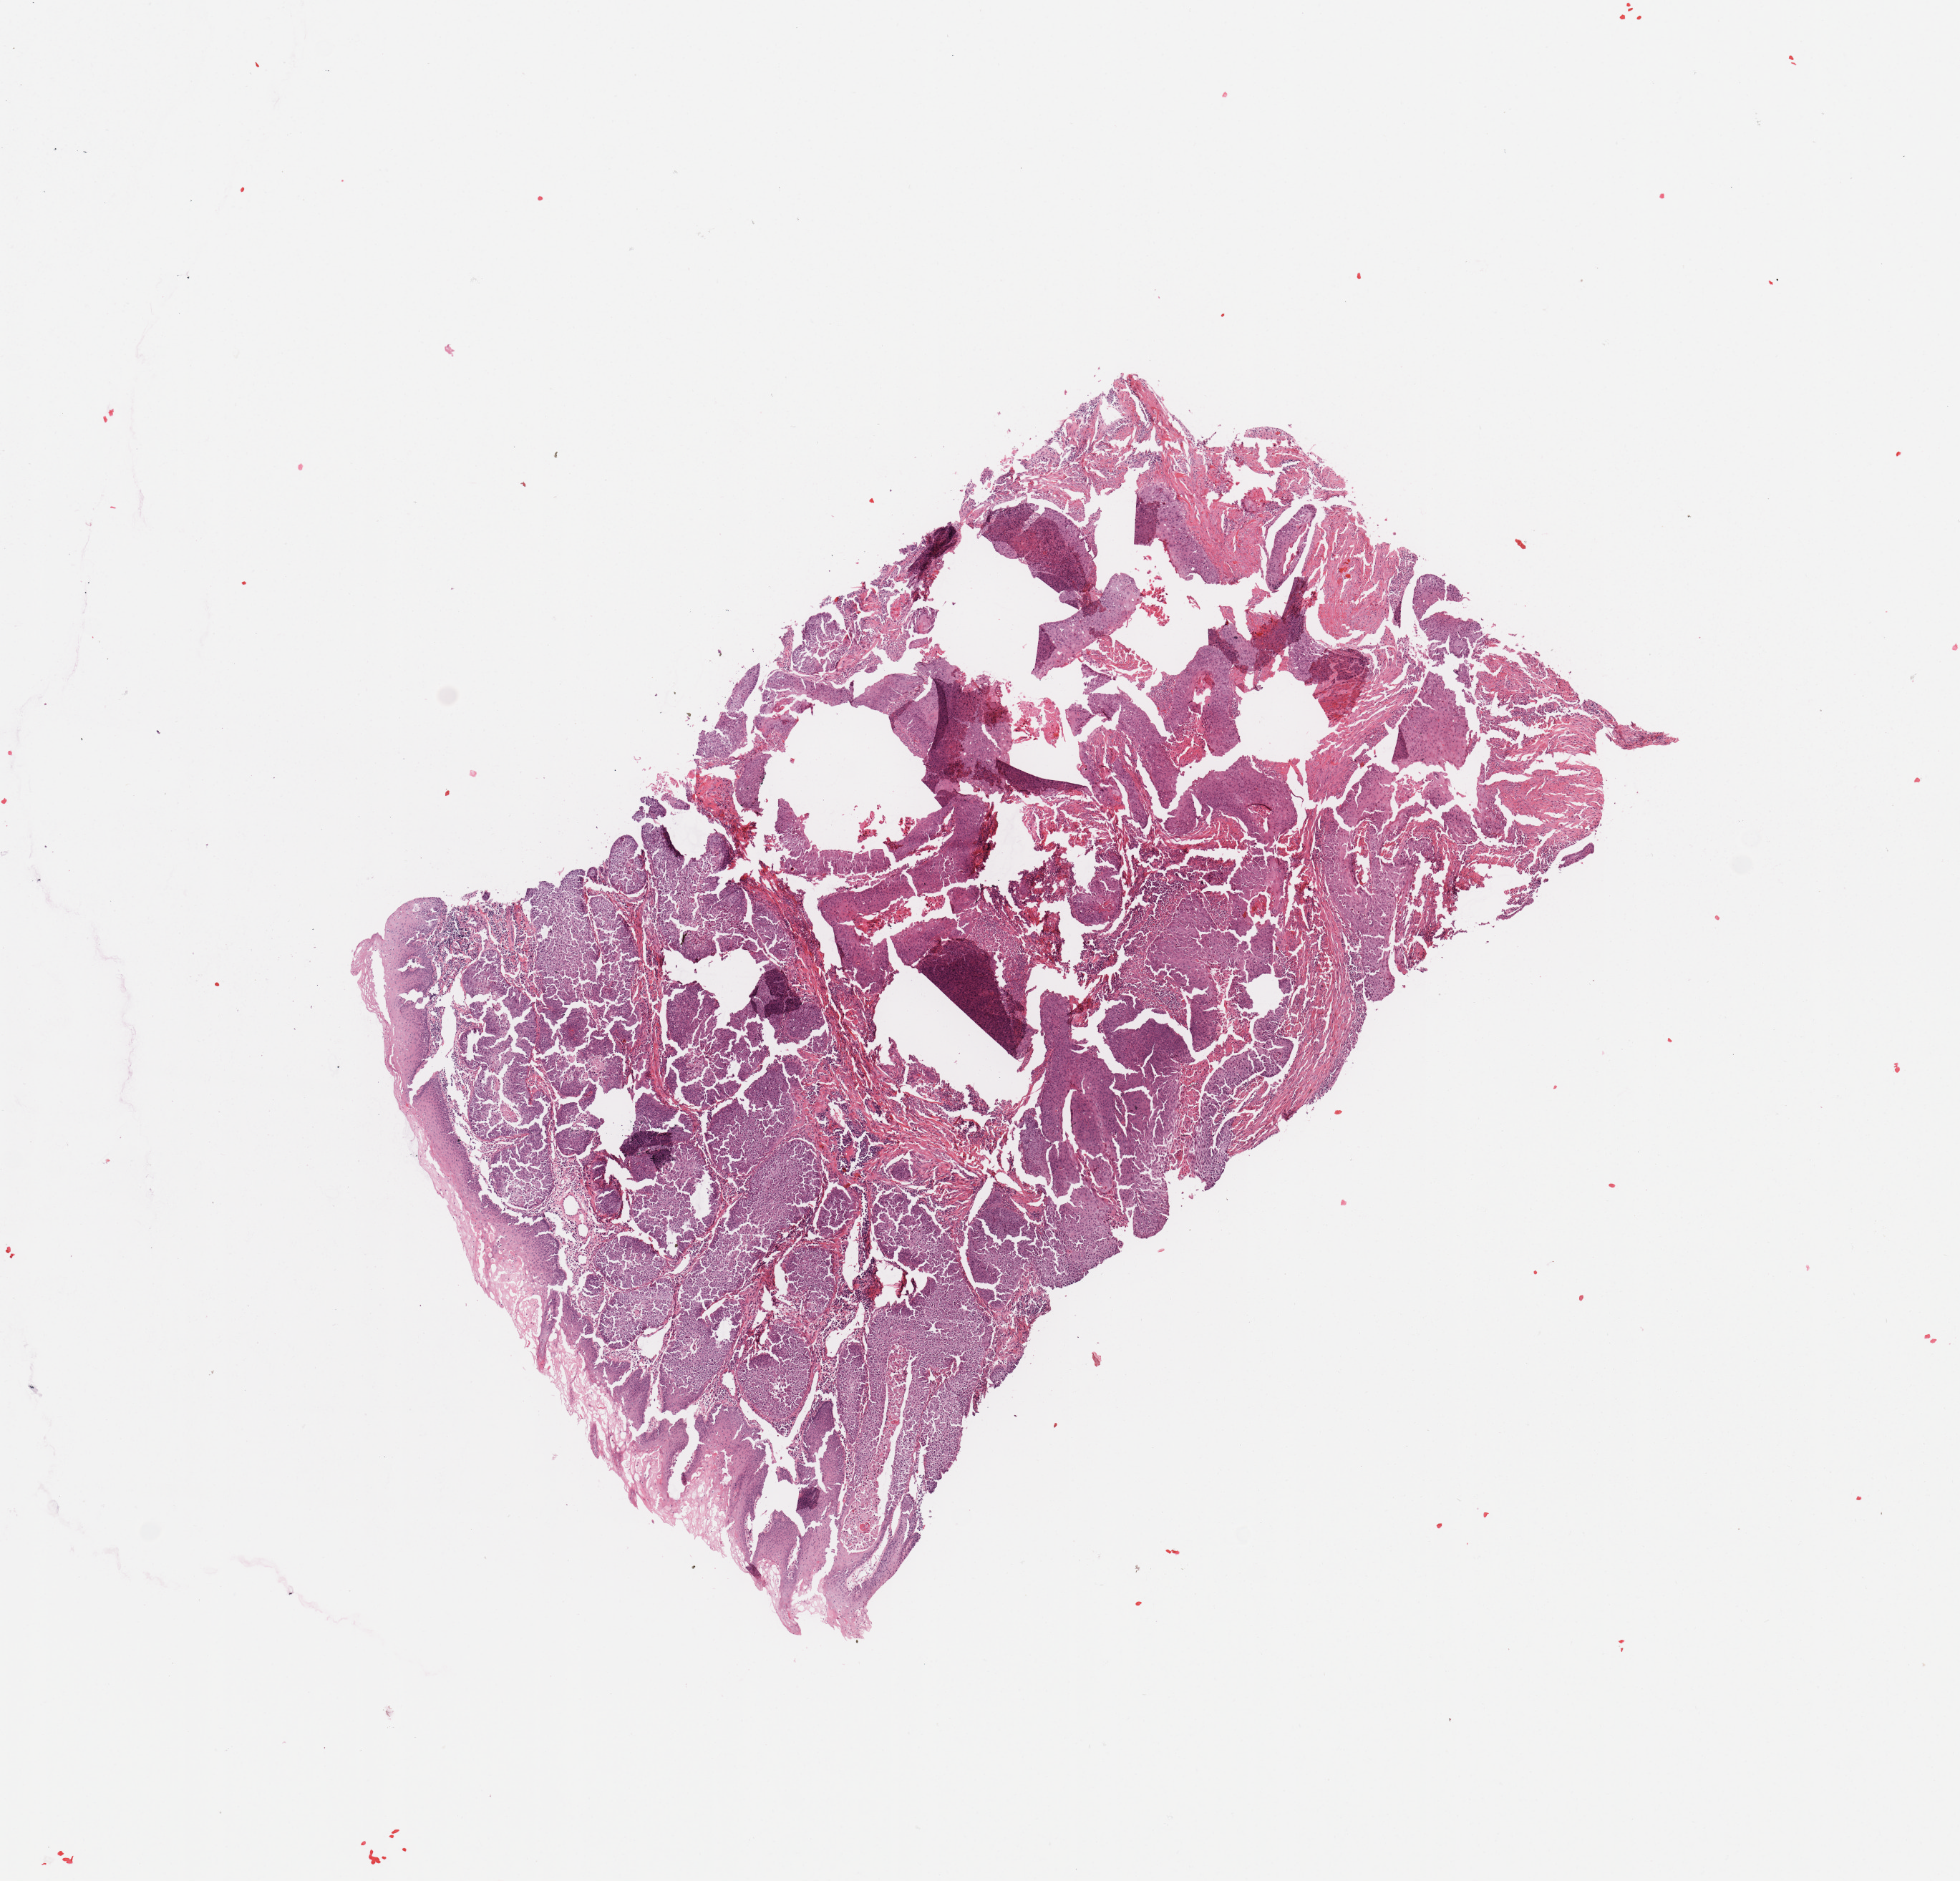
H&E-stained whole-slide image, whole scanned area (about 10.8 x 10.4 mm, acquisition: 20x scan) shown as a low-resolution overview. Tumour tissue sample, sampled site: larynx. Patient: male, age 55 years. Histologic grade: G1 (well differentiated). Pathologist review of this section (percent, as recorded): tumour nuclei 85%, necrosis 5%.
AJCC pathologic stage: IVA. Diagnosis: Squamous cell carcinoma, NOS (larynx, NOS).